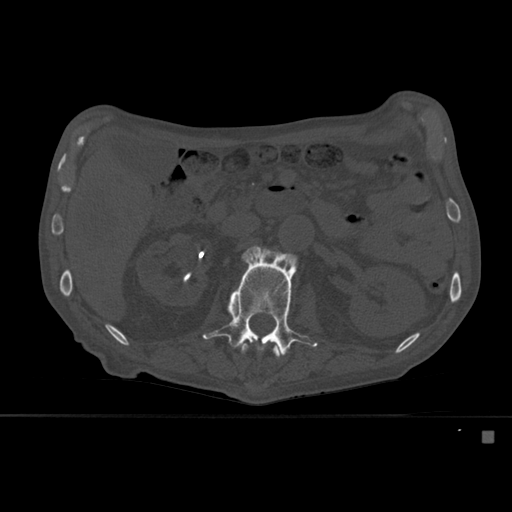
CT including the spine, one axial slice; position 238 of 527 along the scan axis; bone window (W 1800 / L 400 HU); 1.5 mm slice thickness; 512 × 512 image matrix. Male patient, age 78 years. Case-level facts recorded for this patient, not image findings: primary cancer: prostate.
Outlined on this slice (semi-automatically segmented with operator editing):
- L1 vertebra: box from (x=240, y=343) to (x=282, y=358) px
- L2 vertebra: (x=203, y=246)–(x=318, y=356)